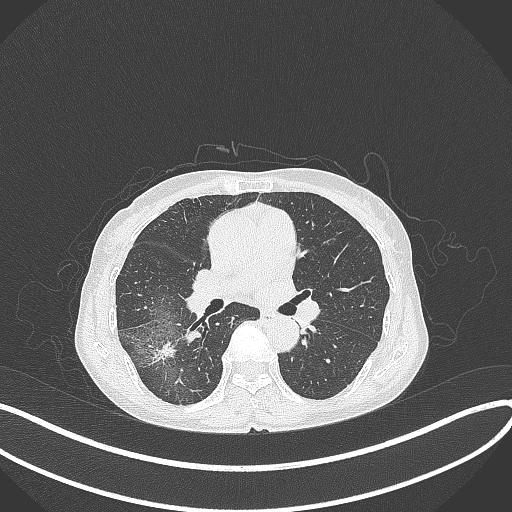
Chest CT, one axial slice; slice 218 of 371 in the series (ordered by position); reconstruction kernel B70f; 120 kVp; lung window (W 1500 / L -600 HU); 1 mm slice thickness; 512 × 512 image matrix, field of view 400 × 400 mm. Female patient, age 69 years. Case-level facts recorded for this patient, not image findings: clinical TNM (as recorded): T1b N0 M0; histopathological grade: G2-3.
Annotated regions visible in this slice (rectangle marked by the reading radiologist):
- lung tumour (recorded histology: adenocarcinoma): bounding box (x1, y1, x2, y2) in pixels: (144, 335, 181, 366)